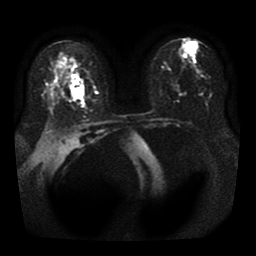
Breast MRI, one axial slice. Slice 20 of 41 in the series (ordered by position). Diffusion-weighted series; image 2 of 4 stored at this slice position (different b-values; order by instance number). 1.5 T. 5 mm slice thickness. 256 × 256 image matrix, field of view 330 × 330 mm. Female patient.
Structures marked on this image (manually delineated by an expert):
- tumour on diffusion-weighted imaging: bounding box (x1, y1, x2, y2) in pixels: (70, 80, 85, 98)